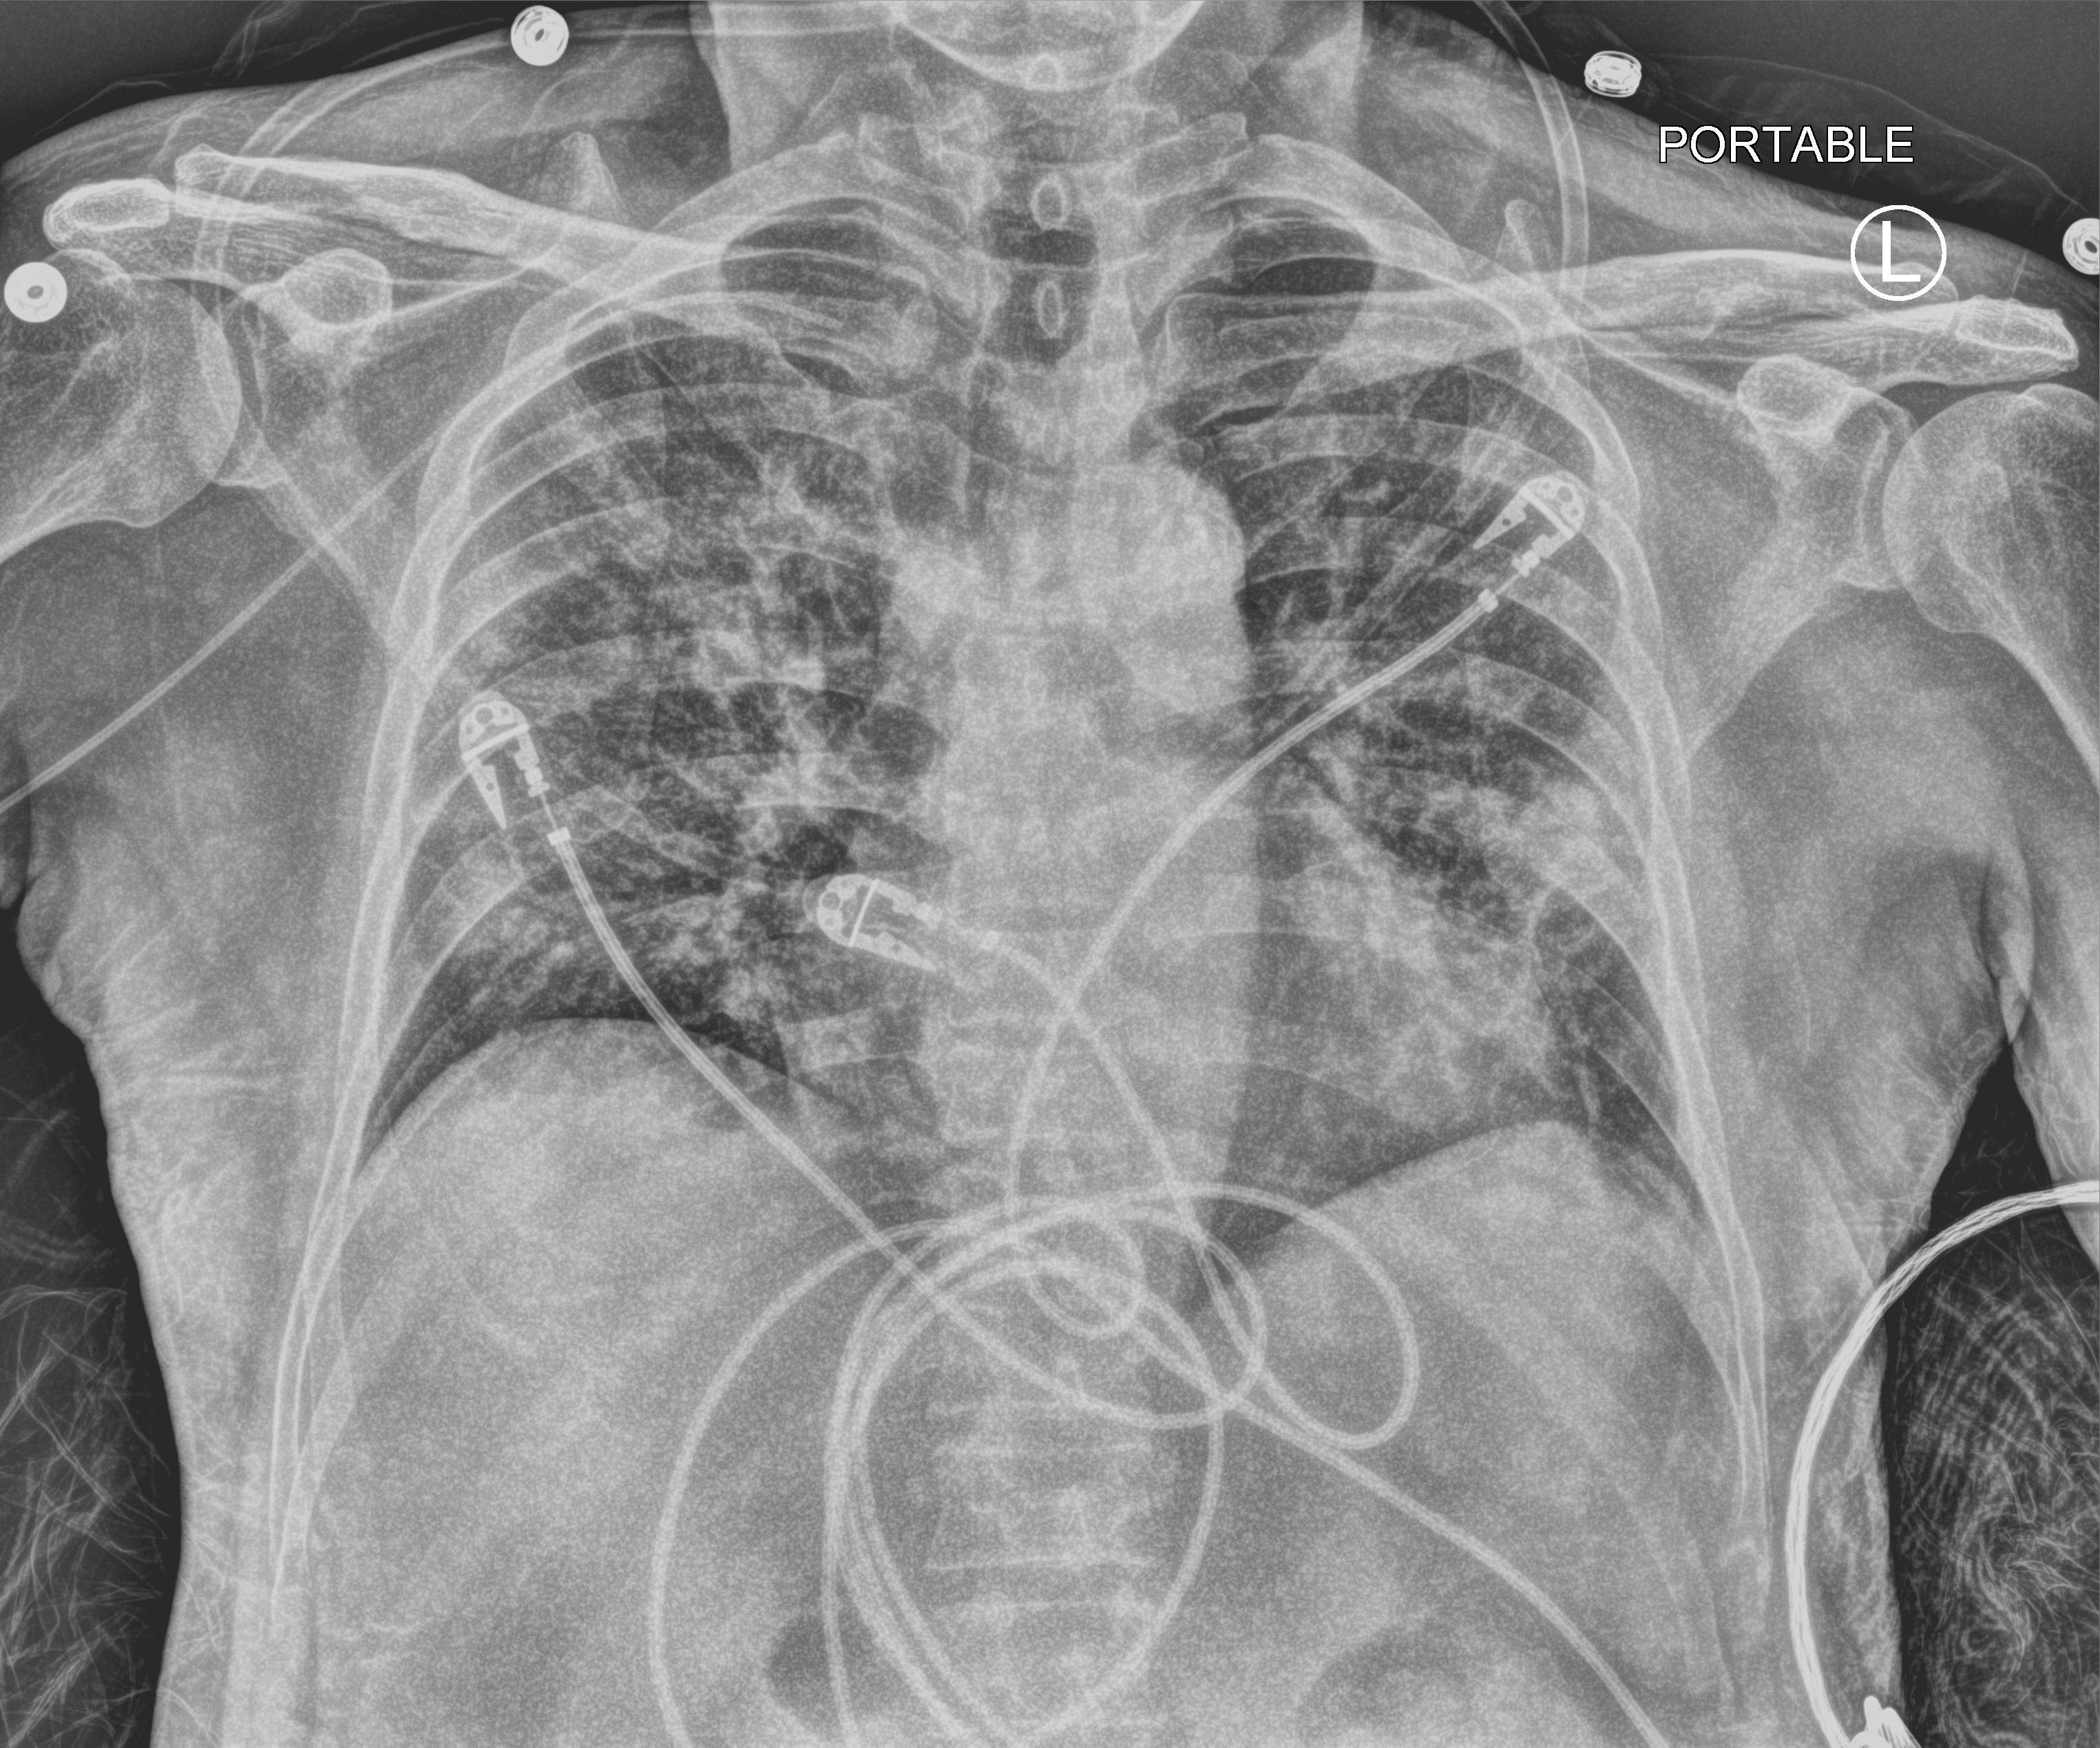
Bedside chest radiograph (computed radiography). Male patient hospitalised with COVID-19, age 60–74 years.
Hospital-stay facts (about this admission, not read from this image; timing relative to this image not recorded): admitted to intensive care during this hospital stay: no; hypertension (admission record): yes.